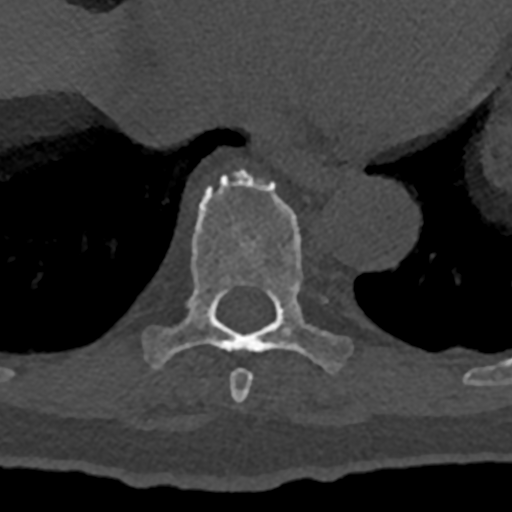
CT including the spine, one axial slice; reconstruction kernel Br40s/3; bone window (W 1800 / L 400 HU); 512 × 512 image matrix, field of view 160 × 160 mm. Patient: male, 74 years. Case-level facts recorded for this patient, not image findings: primary cancer: renal; vertebrae with lytic lesions (as recorded): T10, L1, L2, L3, L4, L5.
Annotated regions visible in this slice (semi-automatic segmentation, software-assisted and operator-edited):
- T8 vertebra: bounding box <230,369,253,404> (left, top, right, bottom; pixels)
- T9 vertebra: <144,169,352,373>